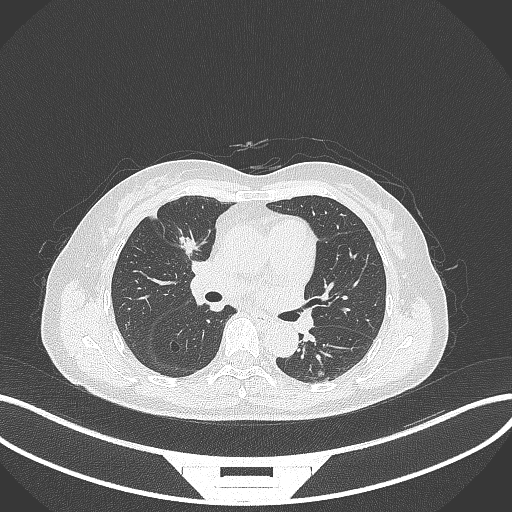
Chest CT, one axial slice. Position 166 of 284 along the scan axis. Reconstruction kernel B70f. 120 kVp. Lung window (W 1500 / L -600 HU). 512 × 512 image matrix, field of view 400 × 400 mm. Female patient, age 51 years. Case-level facts recorded for this patient, not image findings: clinical TNM (as recorded): T1c N0 M0.
Structures marked on this image (rectangle marked by the reading radiologist):
- lung tumour (recorded histology: adenocarcinoma): bounding box [x1, y1, x2, y2] px = [176, 232, 200, 257]